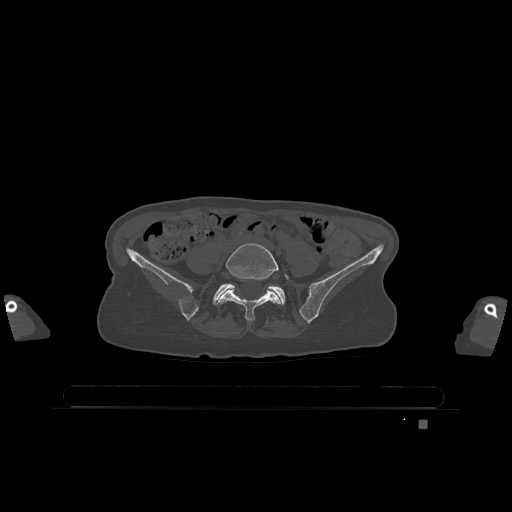
CT including the spine, one axial slice. Position 228 of 1317 along the scan axis. Bone window (W 1800 / L 400 HU). 0.5 mm slice thickness. 512 × 512 image matrix, field of view 500 × 500 mm. Patient: female, 74 years. From the clinical record (not read from this slice): primary cancer: lung; vertebrae with lytic lesions (as recorded): T1, T4, T5, T6, L4, L5.
Outlined on this slice (semi-automatically segmented with operator editing):
- L5 vertebra: bounding box (x1, y1, x2, y2) in pixels: (217, 243, 289, 321)